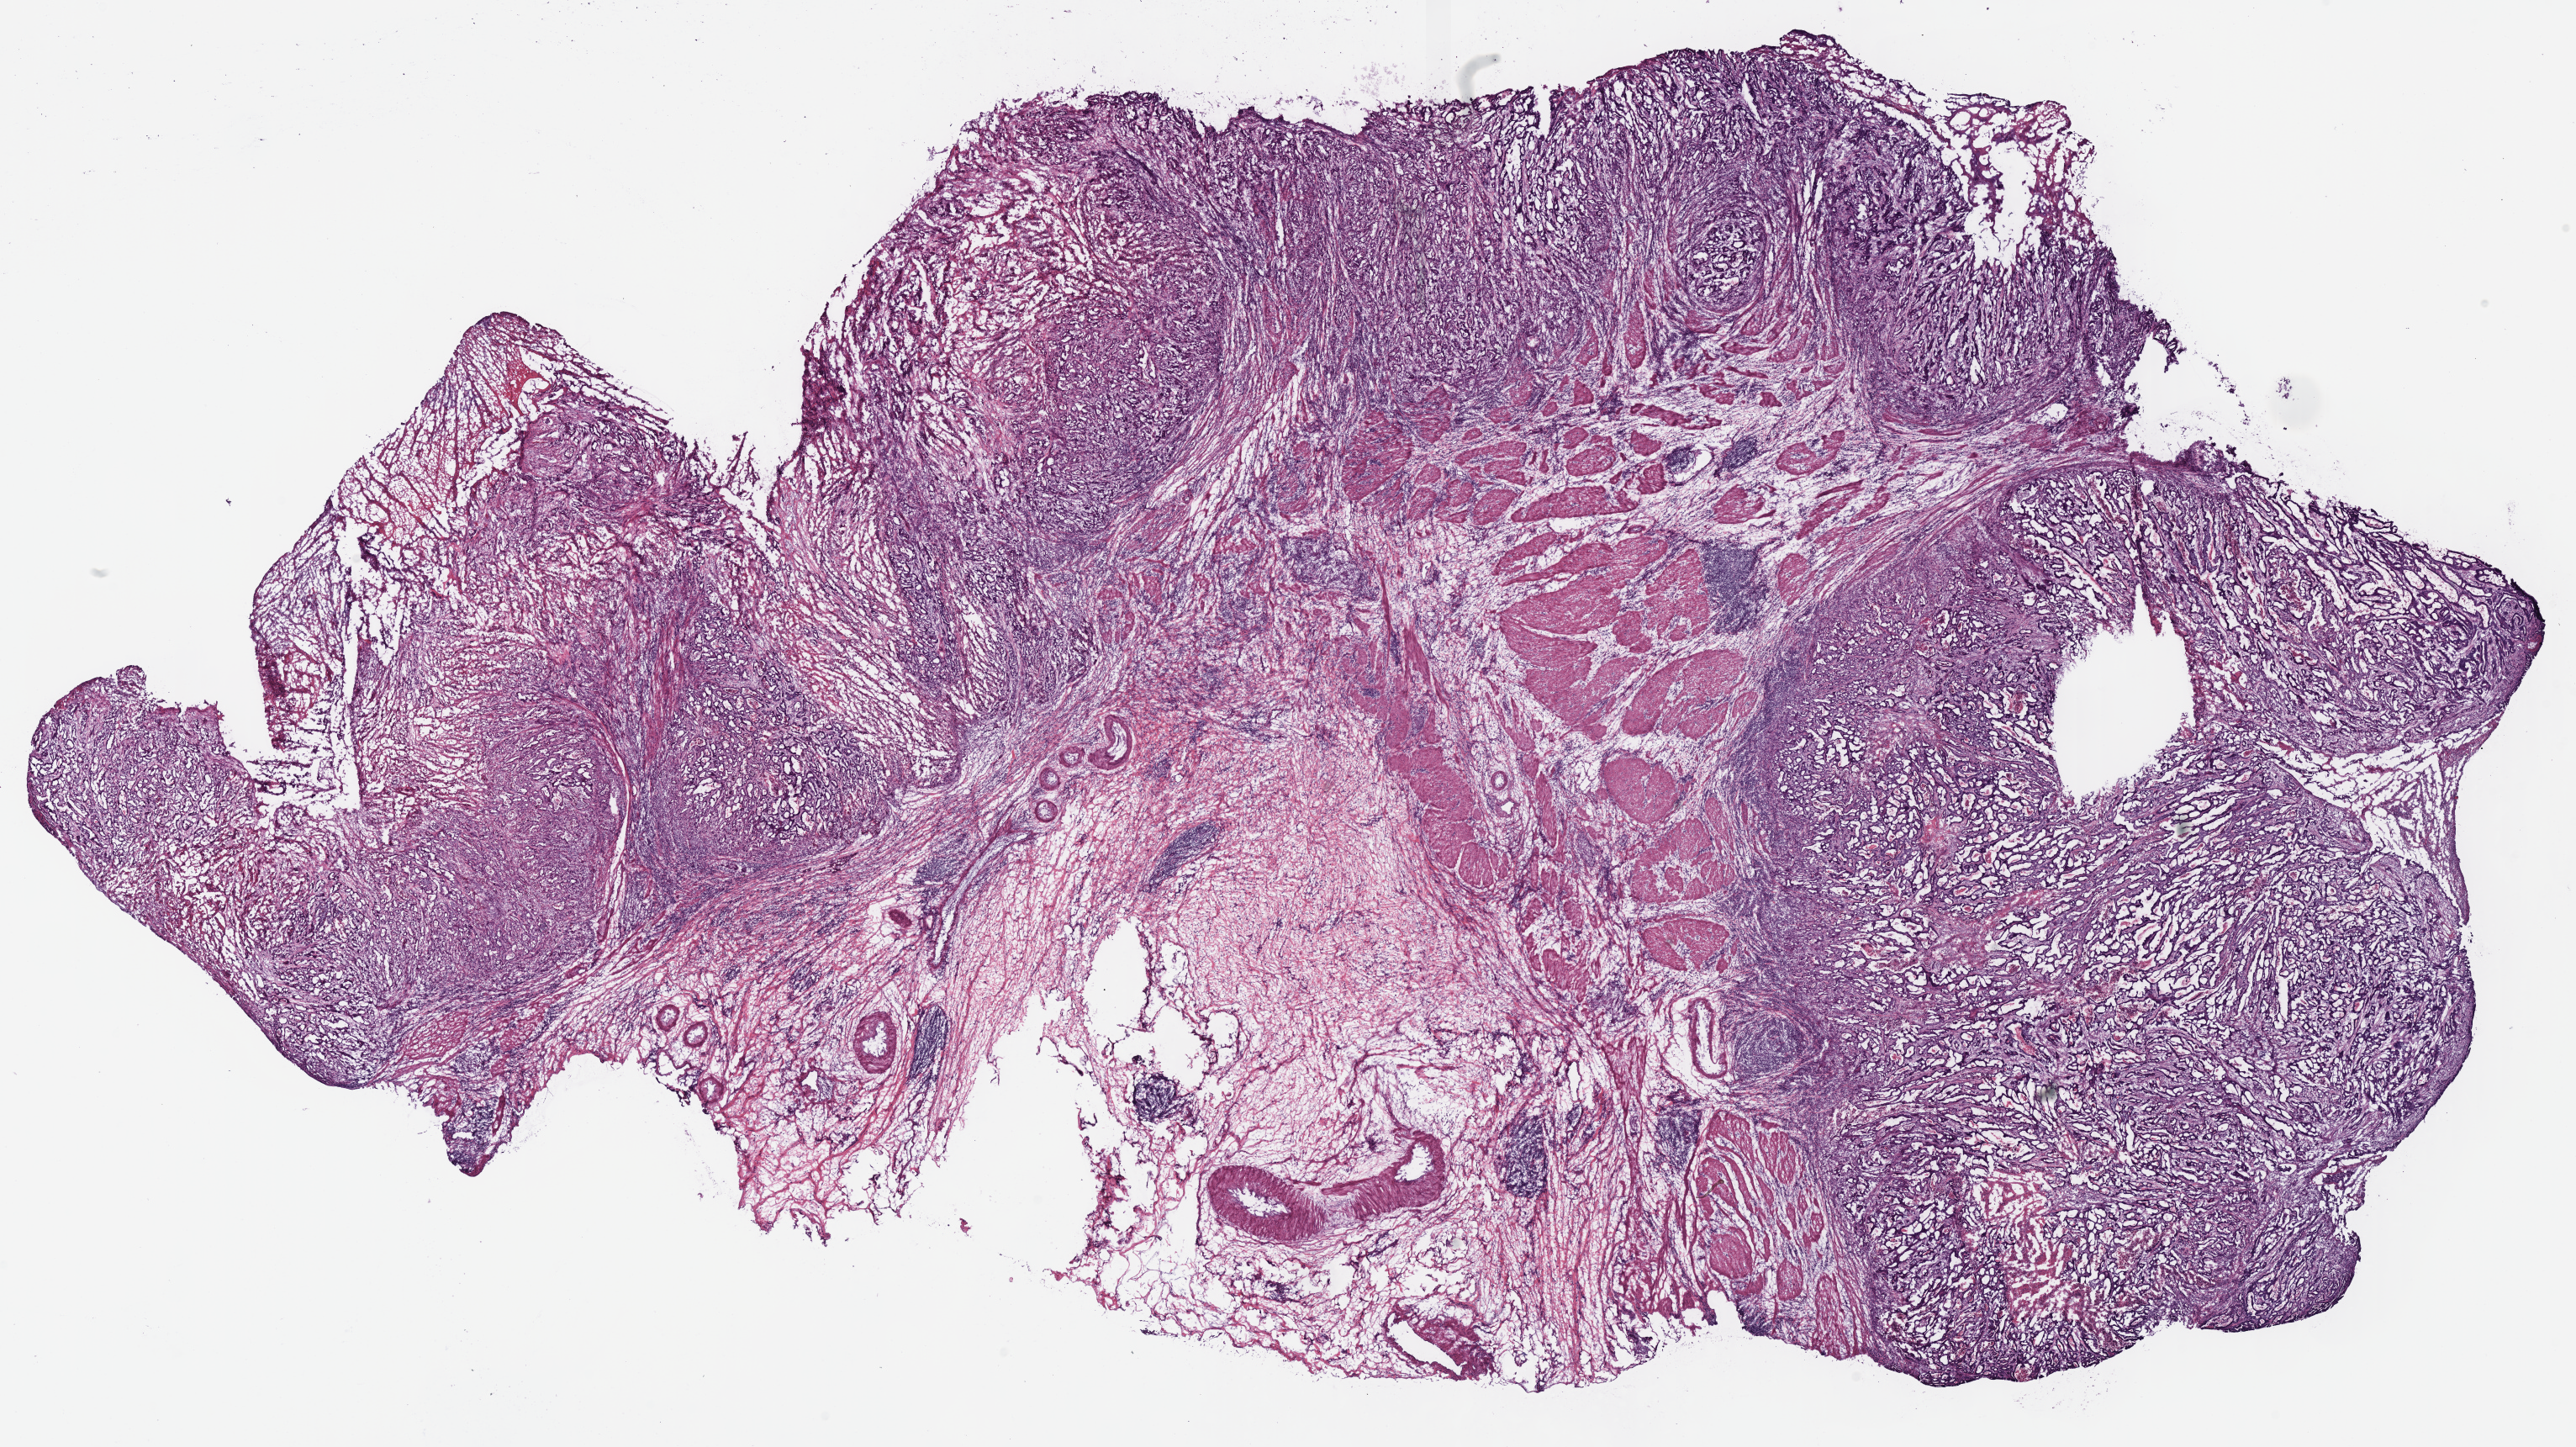
Hematoxylin and eosin (H&E) stained whole-slide image, whole scanned area (about 24.1 x 13.6 mm, acquisition: 40x scan) shown as a low-resolution overview, frozen section, stomach, primary tumour sample. Male patient; age at initial diagnosis 74 years.
Pathologic diagnosis: Adenocarcinoma, intestinal type (body of stomach).